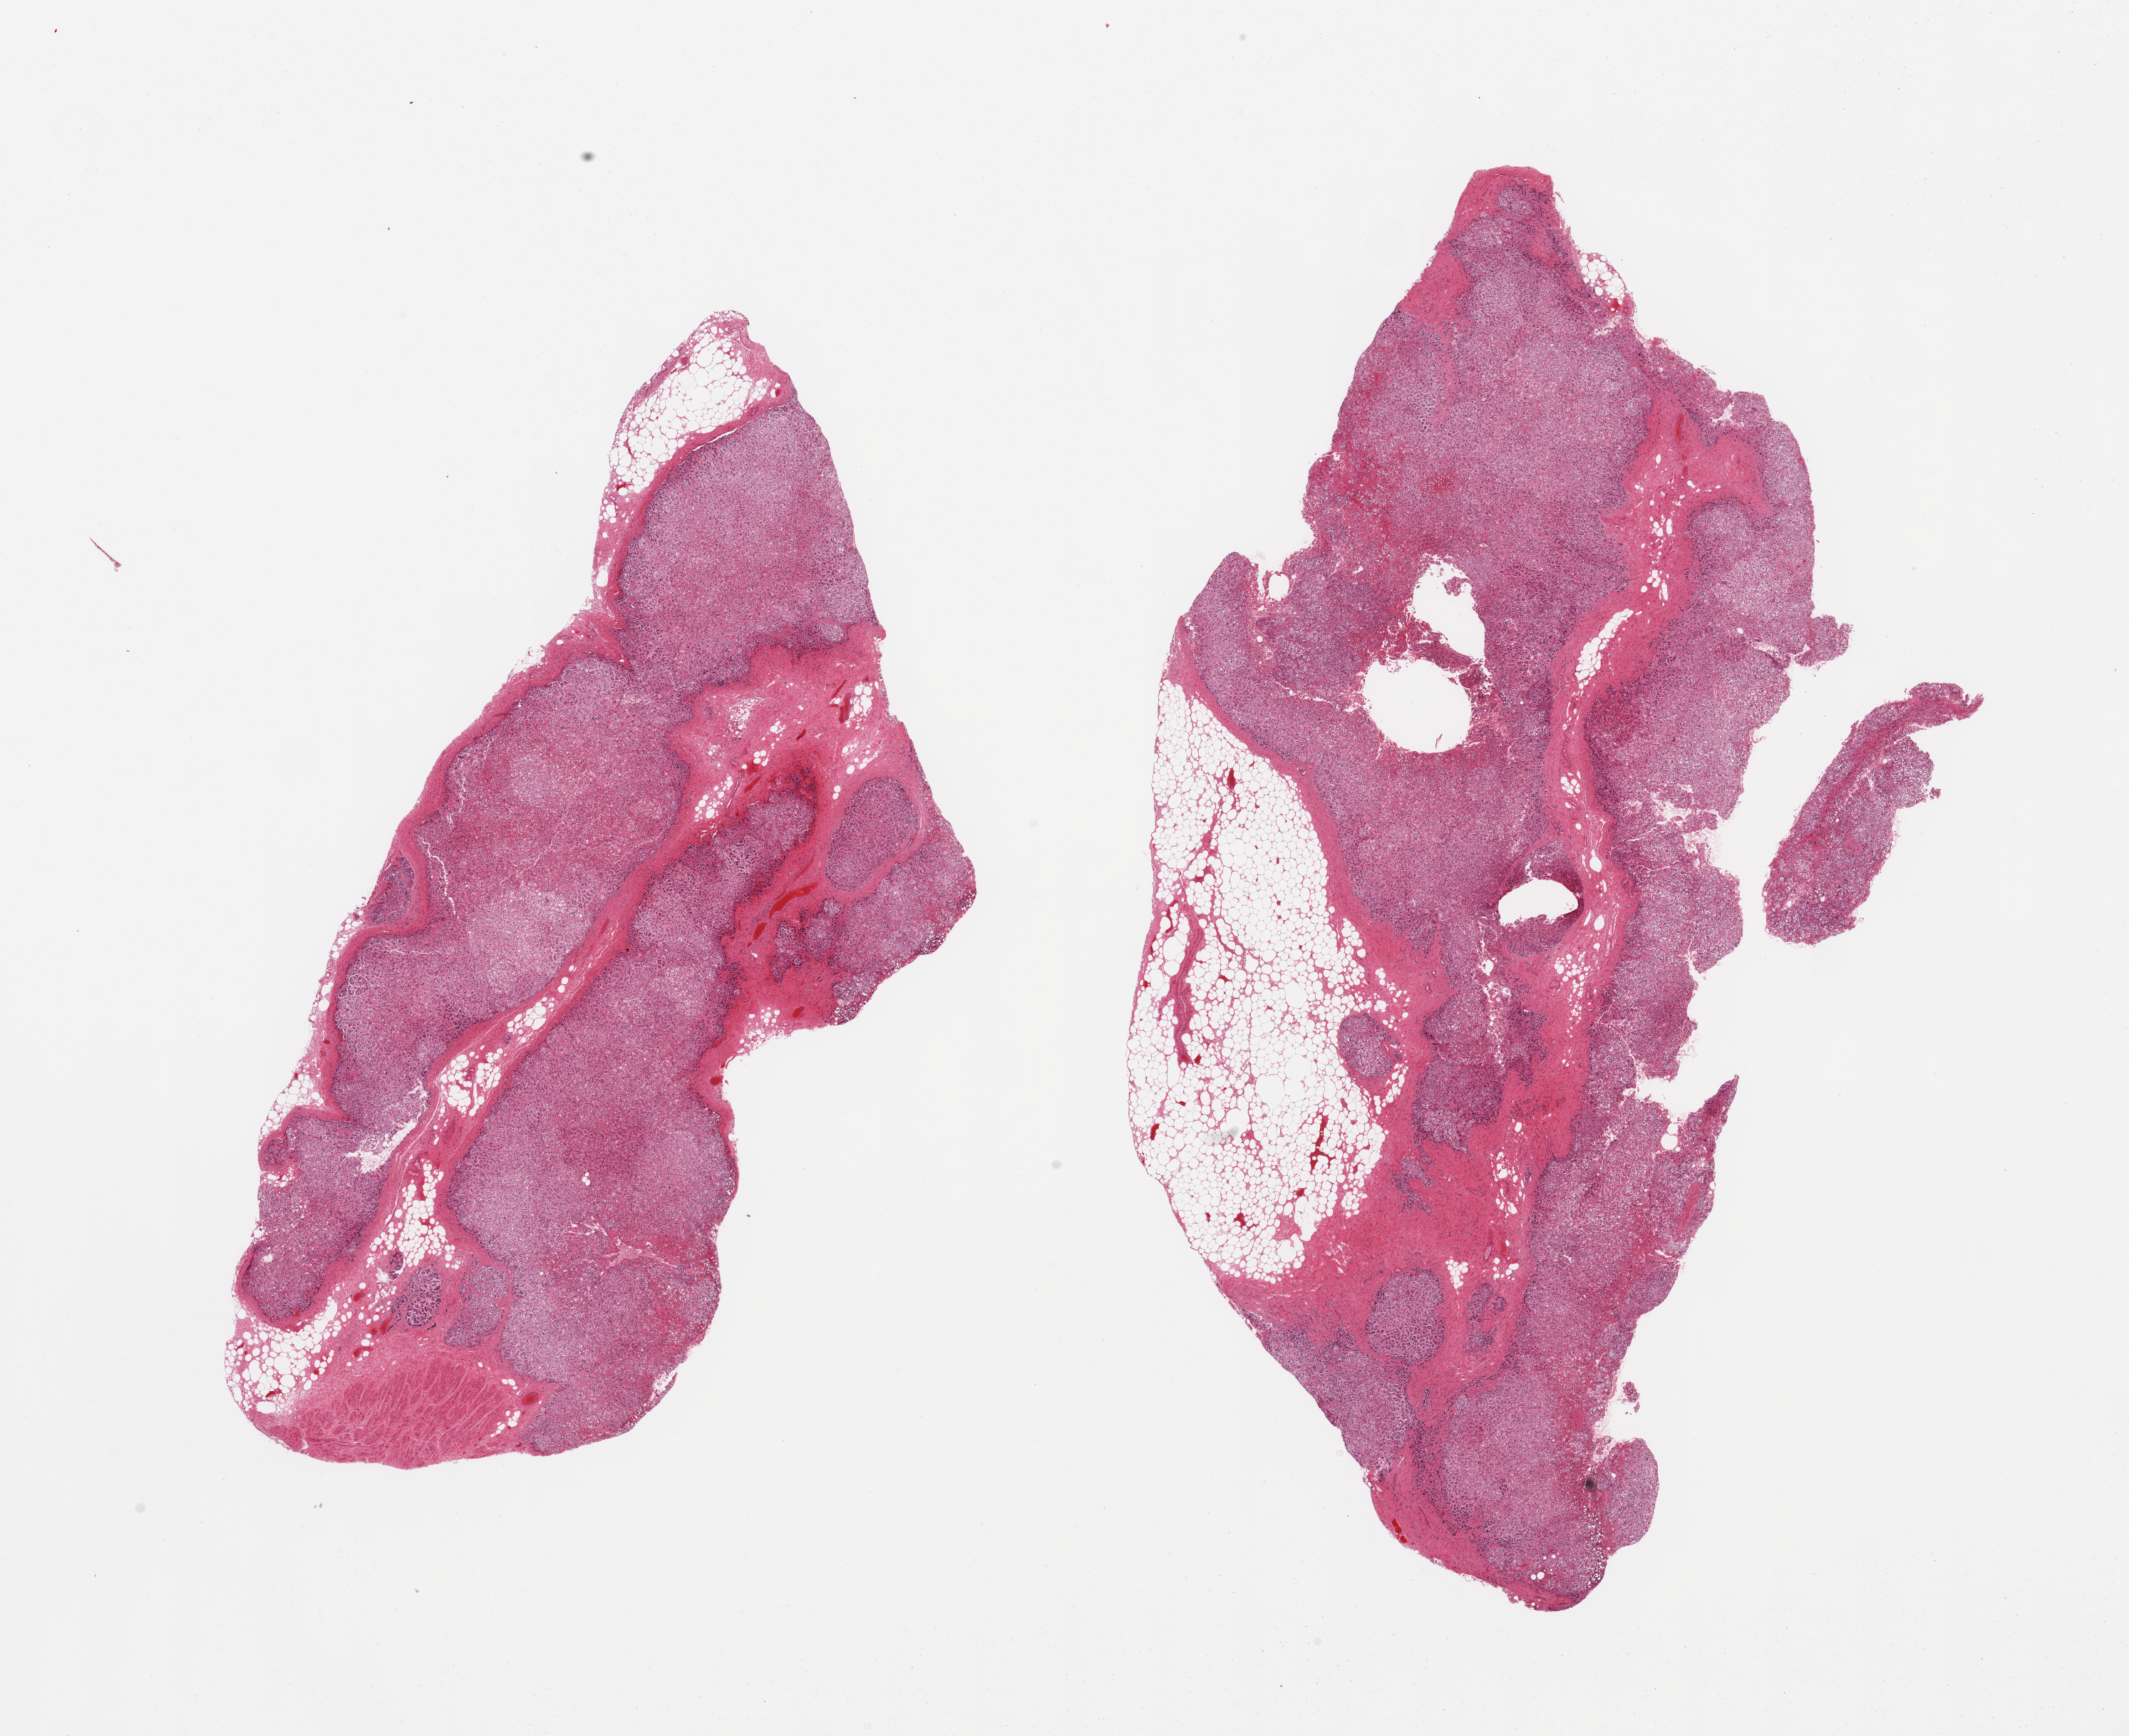
Whole-slide image, haematoxylin and eosin stain, a low-resolution overview of the entire scanned area, about 23.6 x 19.3 mm (acquisition: 20x scan), PAXgene-fixed paraffin-embedded (PFPE) section, sampled site (target tissue): adrenal gland, tissue donor sample. Donor sex: female.
* review note (as recorded): 2 pieces, cortex, focal adherent fat